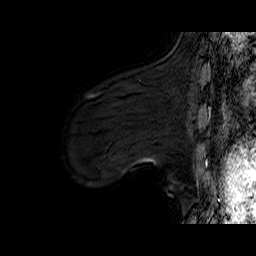
Breast MRI (dynamic contrast-enhanced), one sagittal slice. Dynamic contrast-enhanced series, time point 2 of 6 at this slice position (early post-contrast). 1.5 T. TE 6.4 ms, TR 32.9 ms. 4 mm slice thickness. 256 × 256 image matrix, field of view 200 × 200 mm. Female patient. From the clinical record (not read from this slice): setting: breast cancer imaged before/during neoadjuvant chemotherapy; receptor status: HER2-positive.
Structures marked on this image (semi-automatically segmented with operator editing):
- analysis volume of interest (the breast-tissue region the enhancement analysis was run in; not a lesion): bounding box <82,94,152,149> (left, top, right, bottom; pixels)
- tumour enhancement mask (voxels above the 100 % enhancement threshold inside the analysis volume of interest): <86,94,96,98>